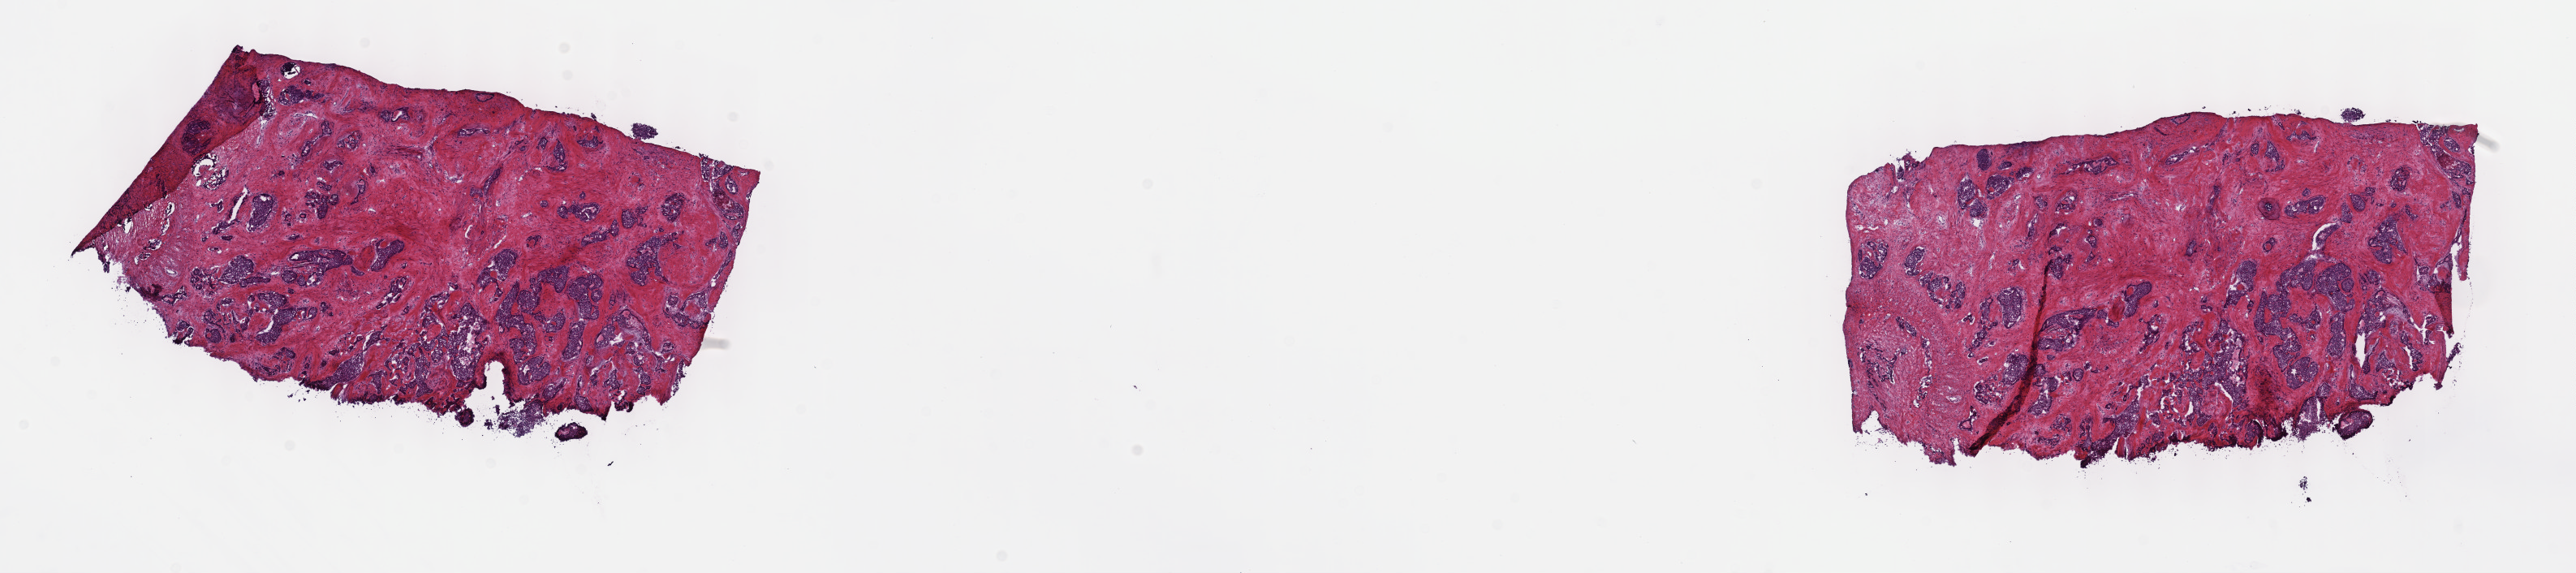
Digitized Hematoxylin and eosin (H&E) stained tissue section (whole slide) — low-resolution overview of the scanned area, about 25.7 x 5.7 mm (from a 40x scan), frozen section from the top of the tissue portion, sample: primary tumour, bile duct. Male patient; age at initial diagnosis 69 years.
Histologic diagnosis: Cholangiocarcinoma.